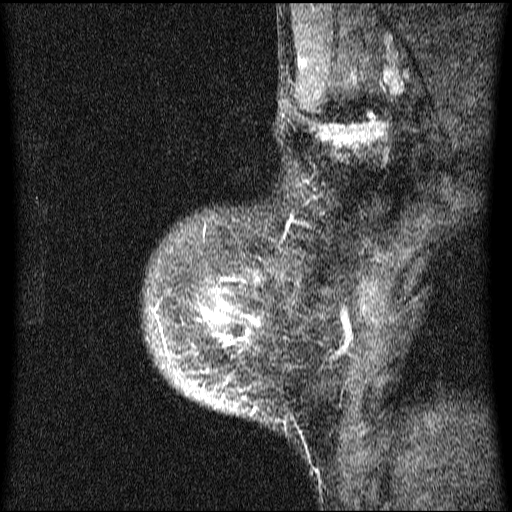
Breast MRI (dynamic contrast-enhanced), one sagittal slice; position 55 of 64 along the scan axis; dynamic contrast-enhanced series, image 2 of 4 at this slice position (ordered by acquisition); 1.5 T; TE 4.2 ms, TR 9.1 ms; 2 mm slice thickness; 512 × 512 image matrix, field of view 180 × 180 mm. Female patient, age 33 years.
Structures marked on this image (semi-automatically segmented with operator editing):
- analysis volume of interest (the breast-tissue region the enhancement analysis was run in; not a lesion): bounding box (x1, y1, x2, y2) in pixels: (145, 181, 326, 434)
- tumour enhancement mask (voxels above the 70 % enhancement threshold inside the analysis volume of interest): (155, 278, 260, 413)